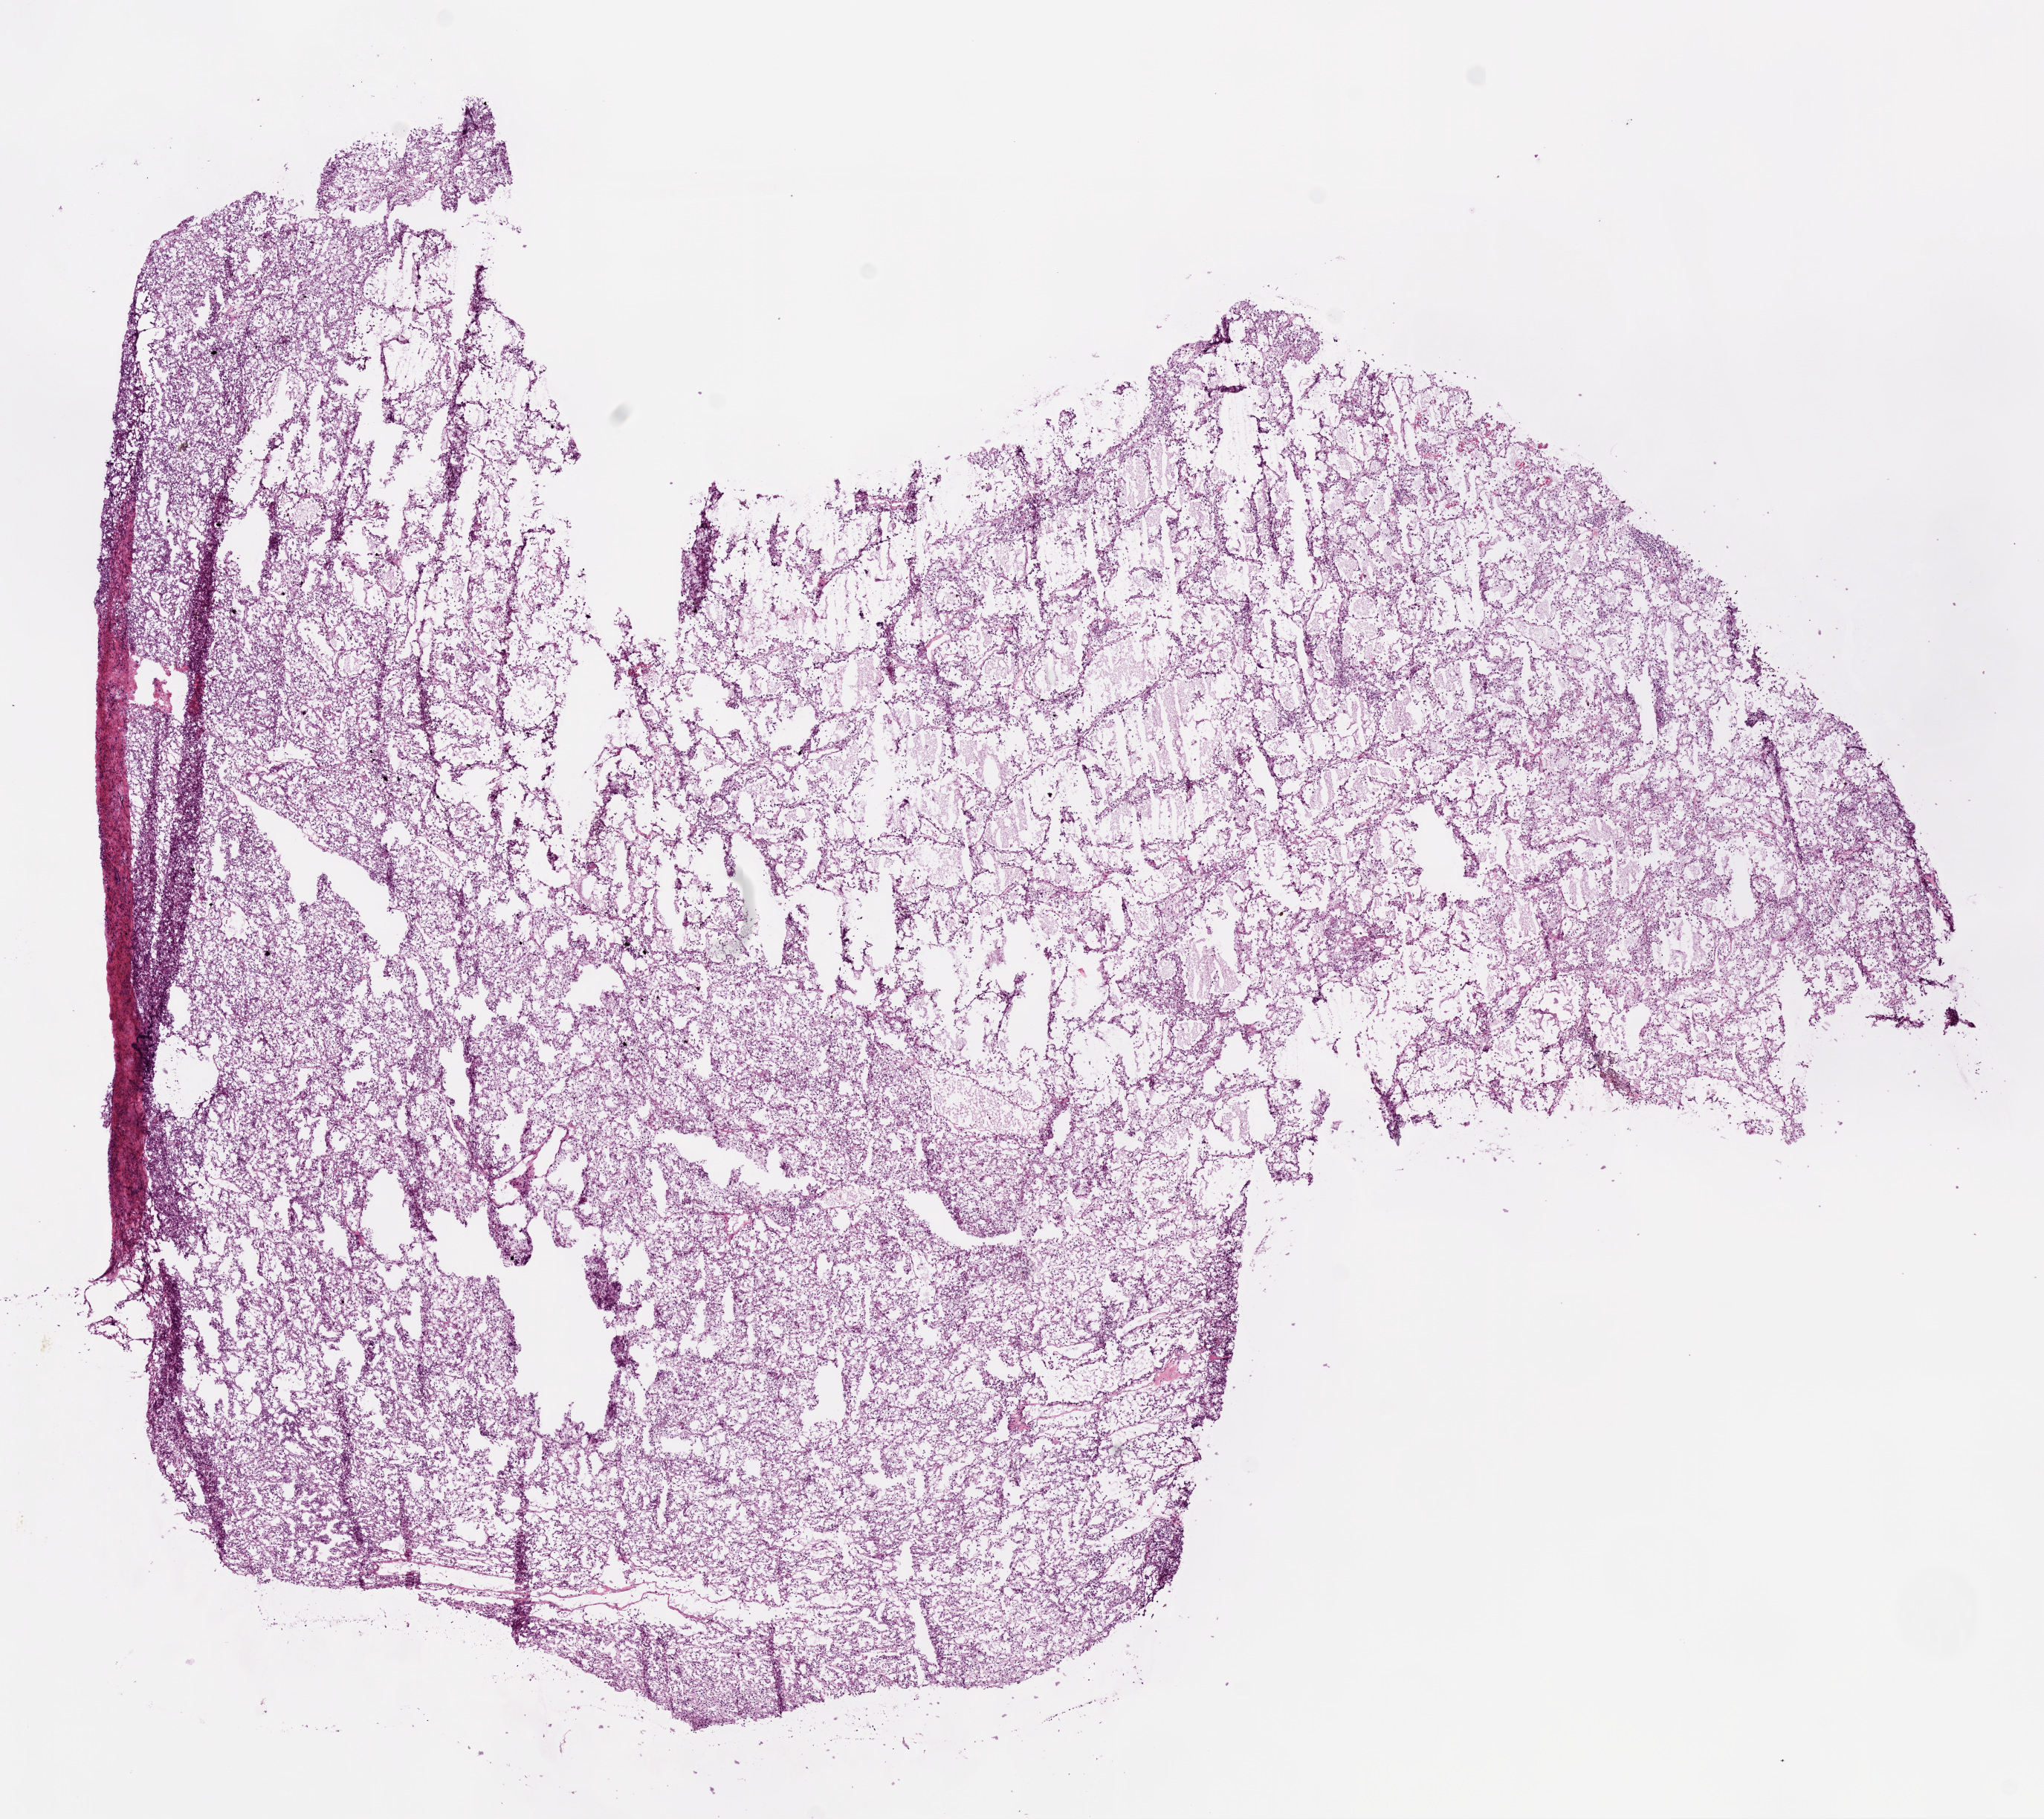
Whole-slide histology image, H&E, low-resolution overview of the scanned area, about 11.0 x 9.8 mm (slide scanned at 20x); frozen section from the bottom of the tissue portion; primary tumour sample from the kidney. Female, age 66 years at initial diagnosis. Histologic grade: G3 (poorly differentiated). Slide review estimates, as recorded: tumour cells 95%, tumour nuclei 85%, normal cells 0%, stromal cells 5%, necrosis 0%.
TNM: T3b N0 M0. Diagnosis: Clear cell adenocarcinoma, NOS. AJCC pathologic stage: III (6th edition).